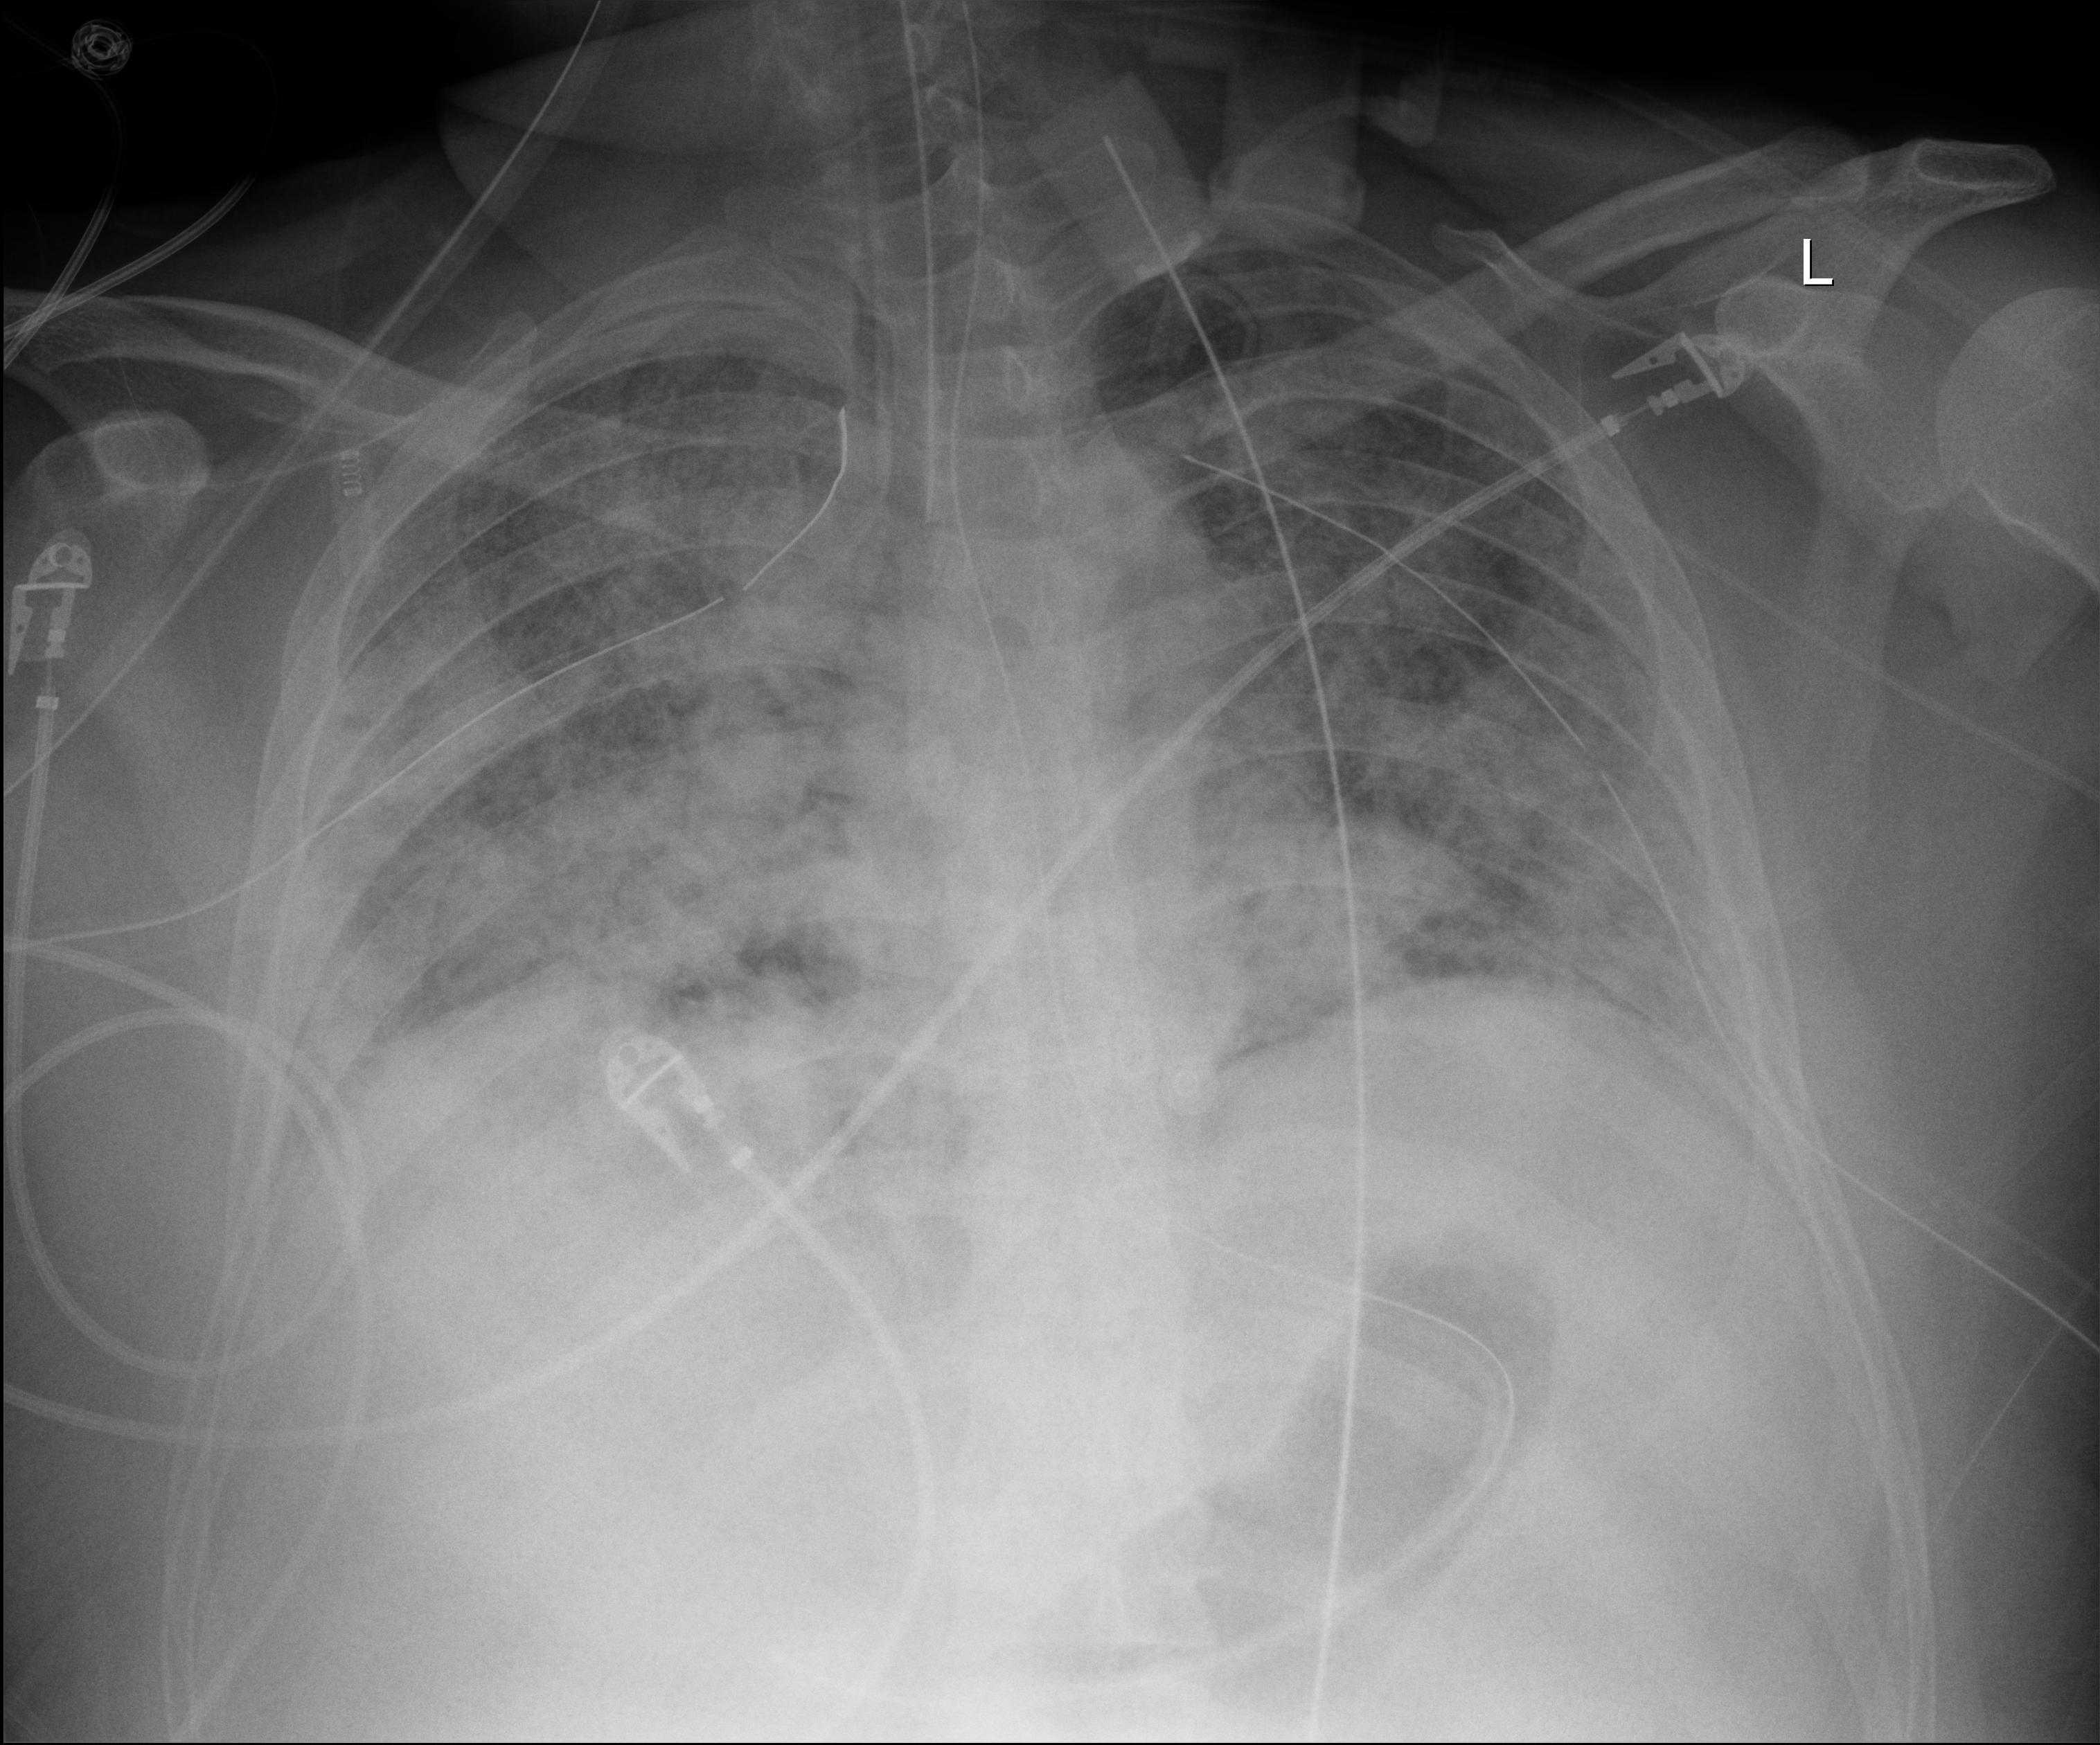
Chest X-ray (portable), anteroposterior (AP) projection. Male patient hospitalised with COVID-19, age 18–59 years.
From the hospital-stay record, not from the radiograph (when in the stay this image was taken is not recorded):
- length of hospital stay: 63 days
- admitted to intensive care during this hospital stay: yes